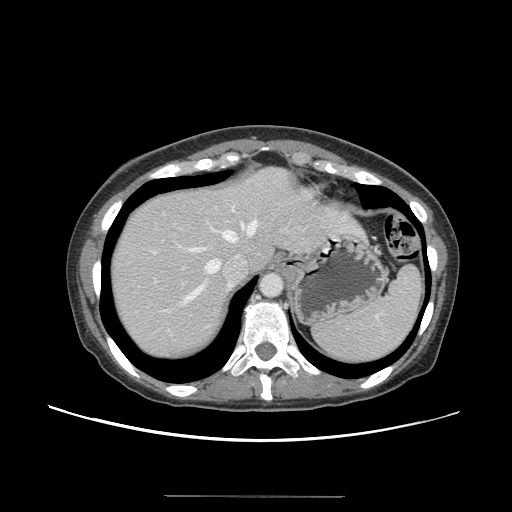
Contrast-enhanced abdominal CT, one axial slice; slice 119 of 144 in the series (ordered by position); intravenous contrast given; soft-tissue window (W 400 / L 40 HU); 2.5 mm slice thickness; 512 × 512 image matrix, field of view 380 × 380 mm. Female patient, age 53 years. Case-level facts recorded for this patient, not image findings: diagnosis: colorectal cancer liver metastases, imaged before liver resection; multiple liver metastases: yes; largest metastasis: 1.1 cm.
Outlined on this slice (expert manual segmentation):
- hepatic veins: bounding box (x1, y1, x2, y2) in pixels: (184, 220, 257, 302)
- liver: (110, 169, 362, 360)
- planned liver remnant (the part of the liver to remain after resection): (110, 168, 286, 298)
- liver metastasis: (168, 350, 177, 357)